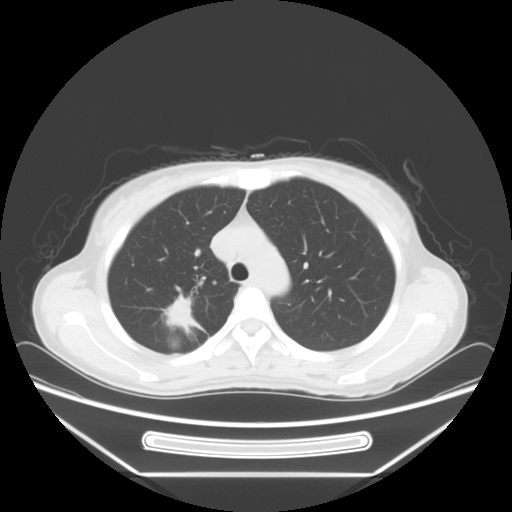
Chest CT, one axial slice; slice 49 of 66 in the series (ordered by position); reconstruction kernel STANDARD; lung window (W 1500 / L -600 HU); 512 × 512 image matrix, field of view 408 × 408 mm. Patient: female, 37 years. Case-level facts recorded for this patient, not image findings: clinical TNM (as recorded): T1c N0 M1.
Annotated regions visible in this slice (bounding box drawn by a radiologist):
- lung tumour (recorded histology: adenocarcinoma): bounding box <164,294,208,330> (left, top, right, bottom; pixels)